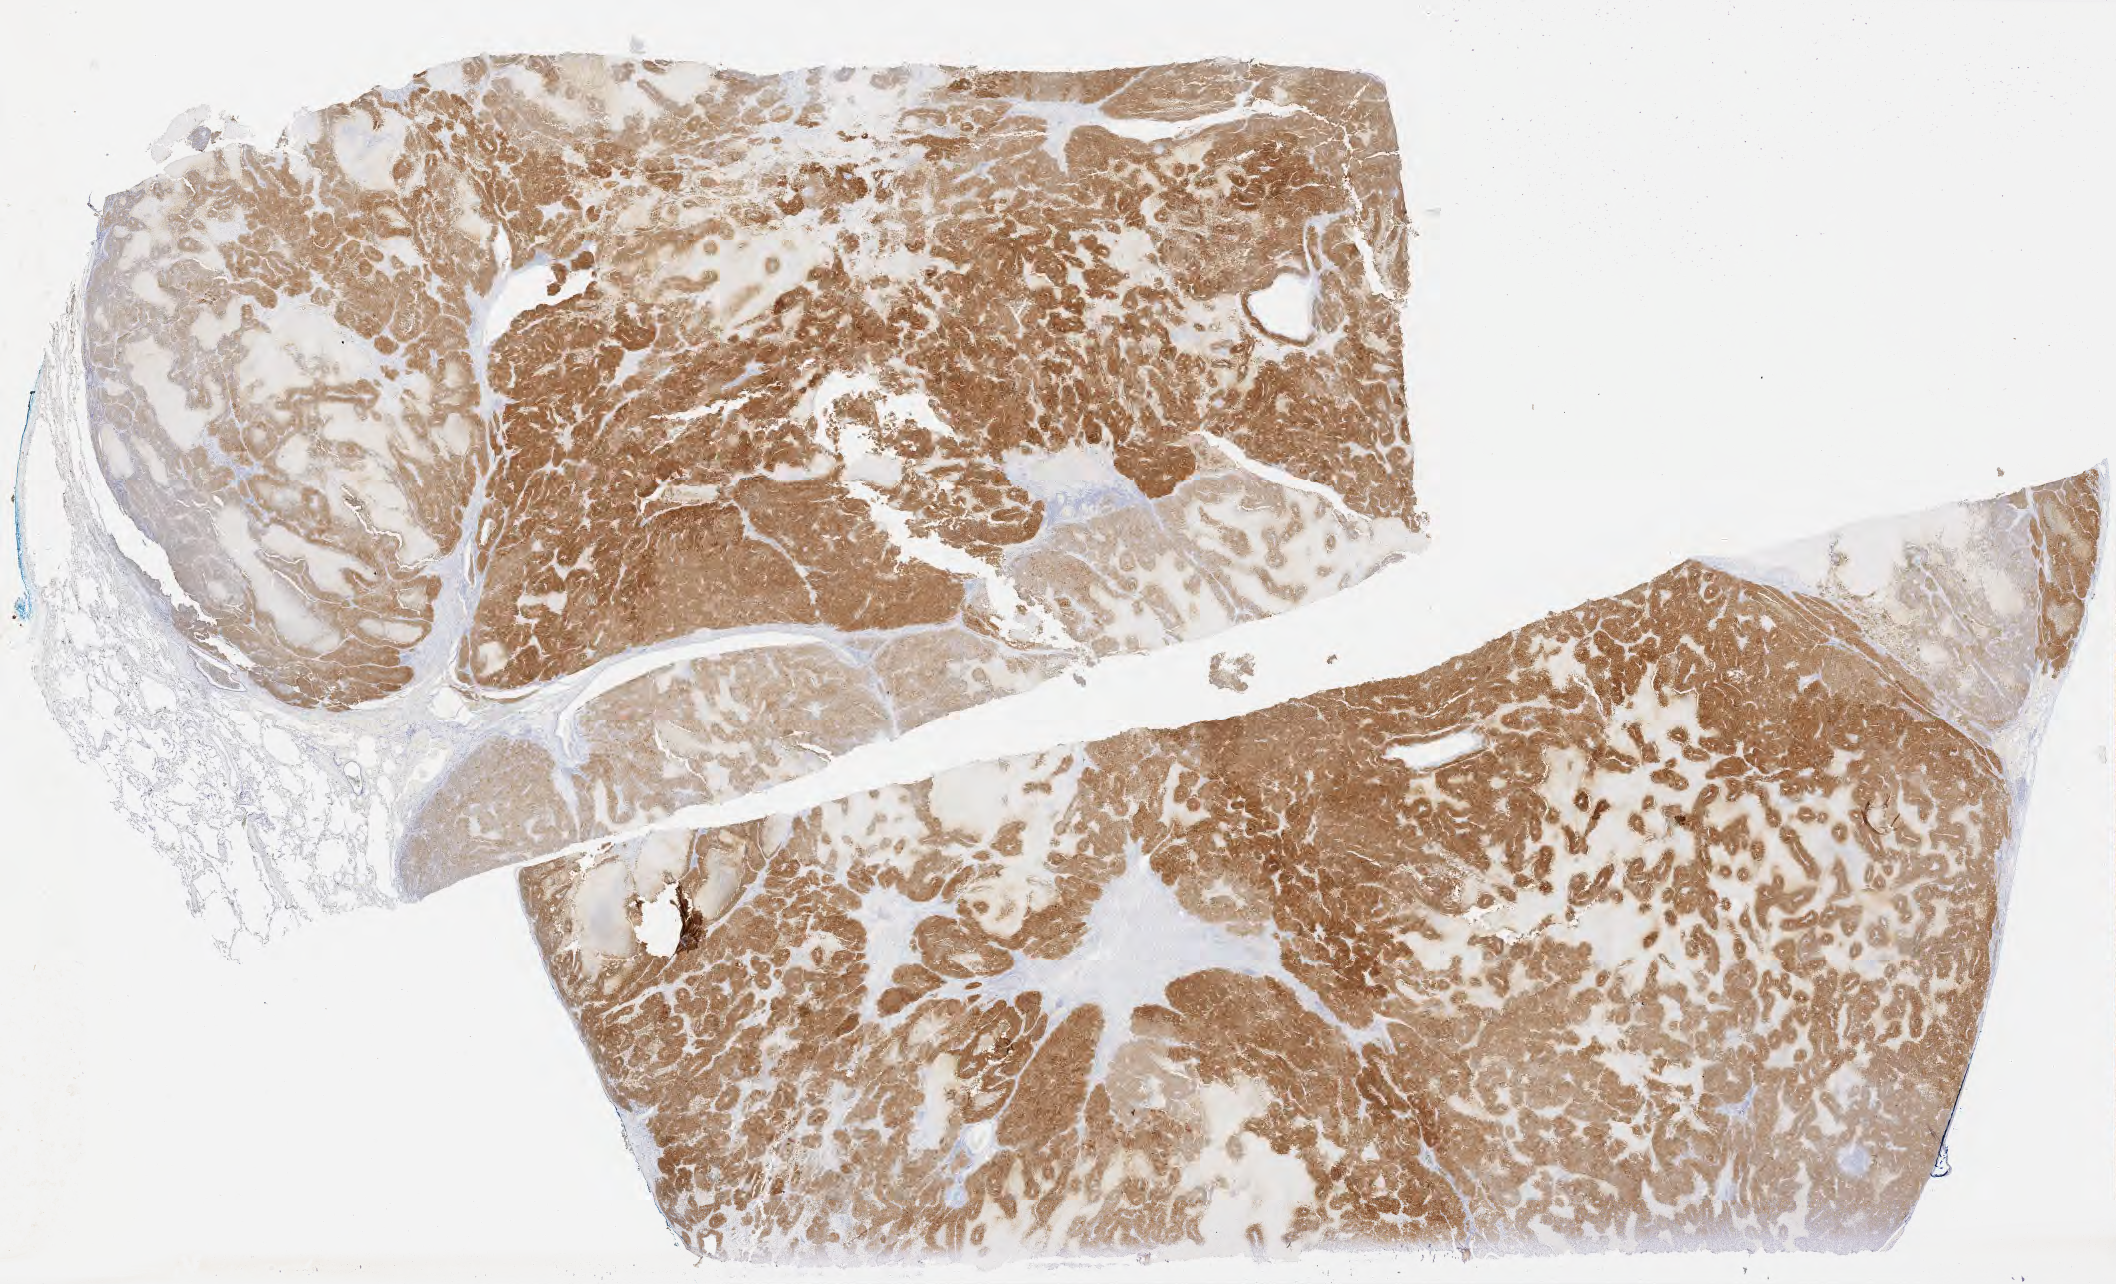
Whole-slide image, immunohistochemical stain for synaptophysin — whole scanned area (about 34.2 x 20.8 mm) shown as a low-resolution overview, tumor tissue, anatomic site: lung. Patient: female, age 61 years.
Diagnosis: Large cell neuroendocrine carcinoma.